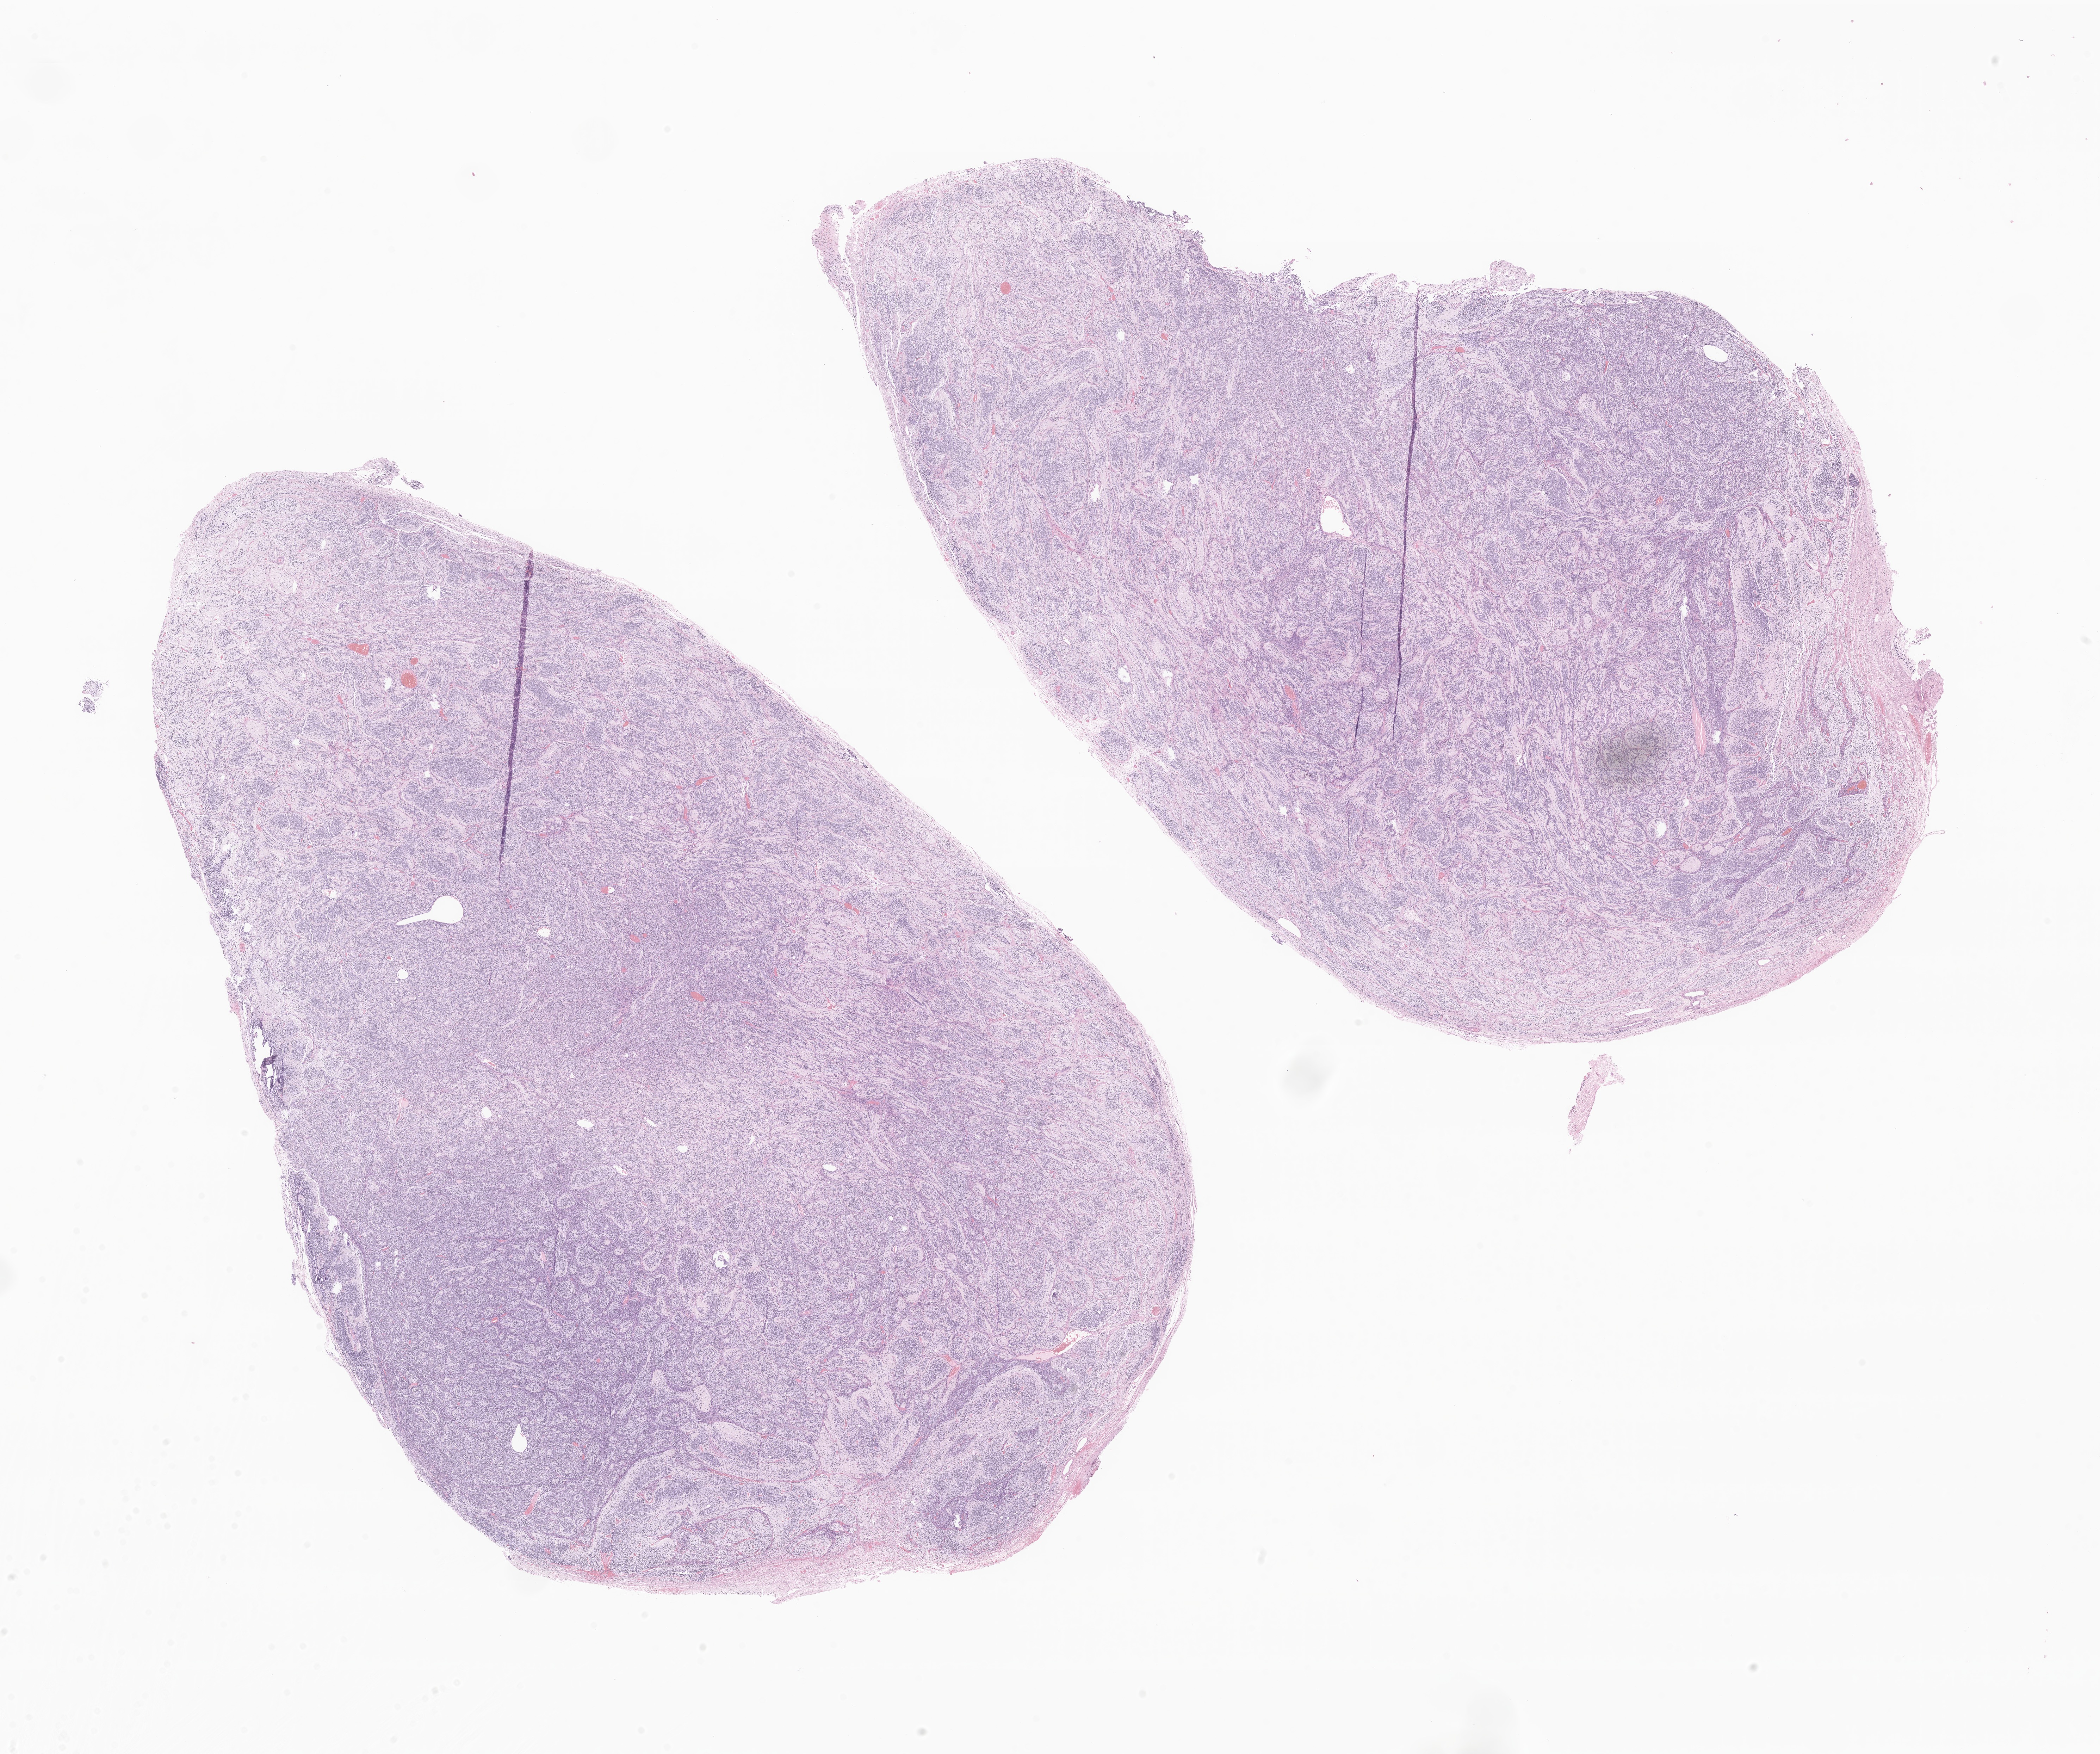
Digitized H&E-stained section of tumor tissue from the brain, whole scanned area (about 25.1 x 21.0 mm) shown as a low-resolution overview, formalin-fixed paraffin-embedded section. Patient: female, age 533 days (about 1.5 years).
Recorded diagnosis: Desmoplastic nodular medulloblastoma.